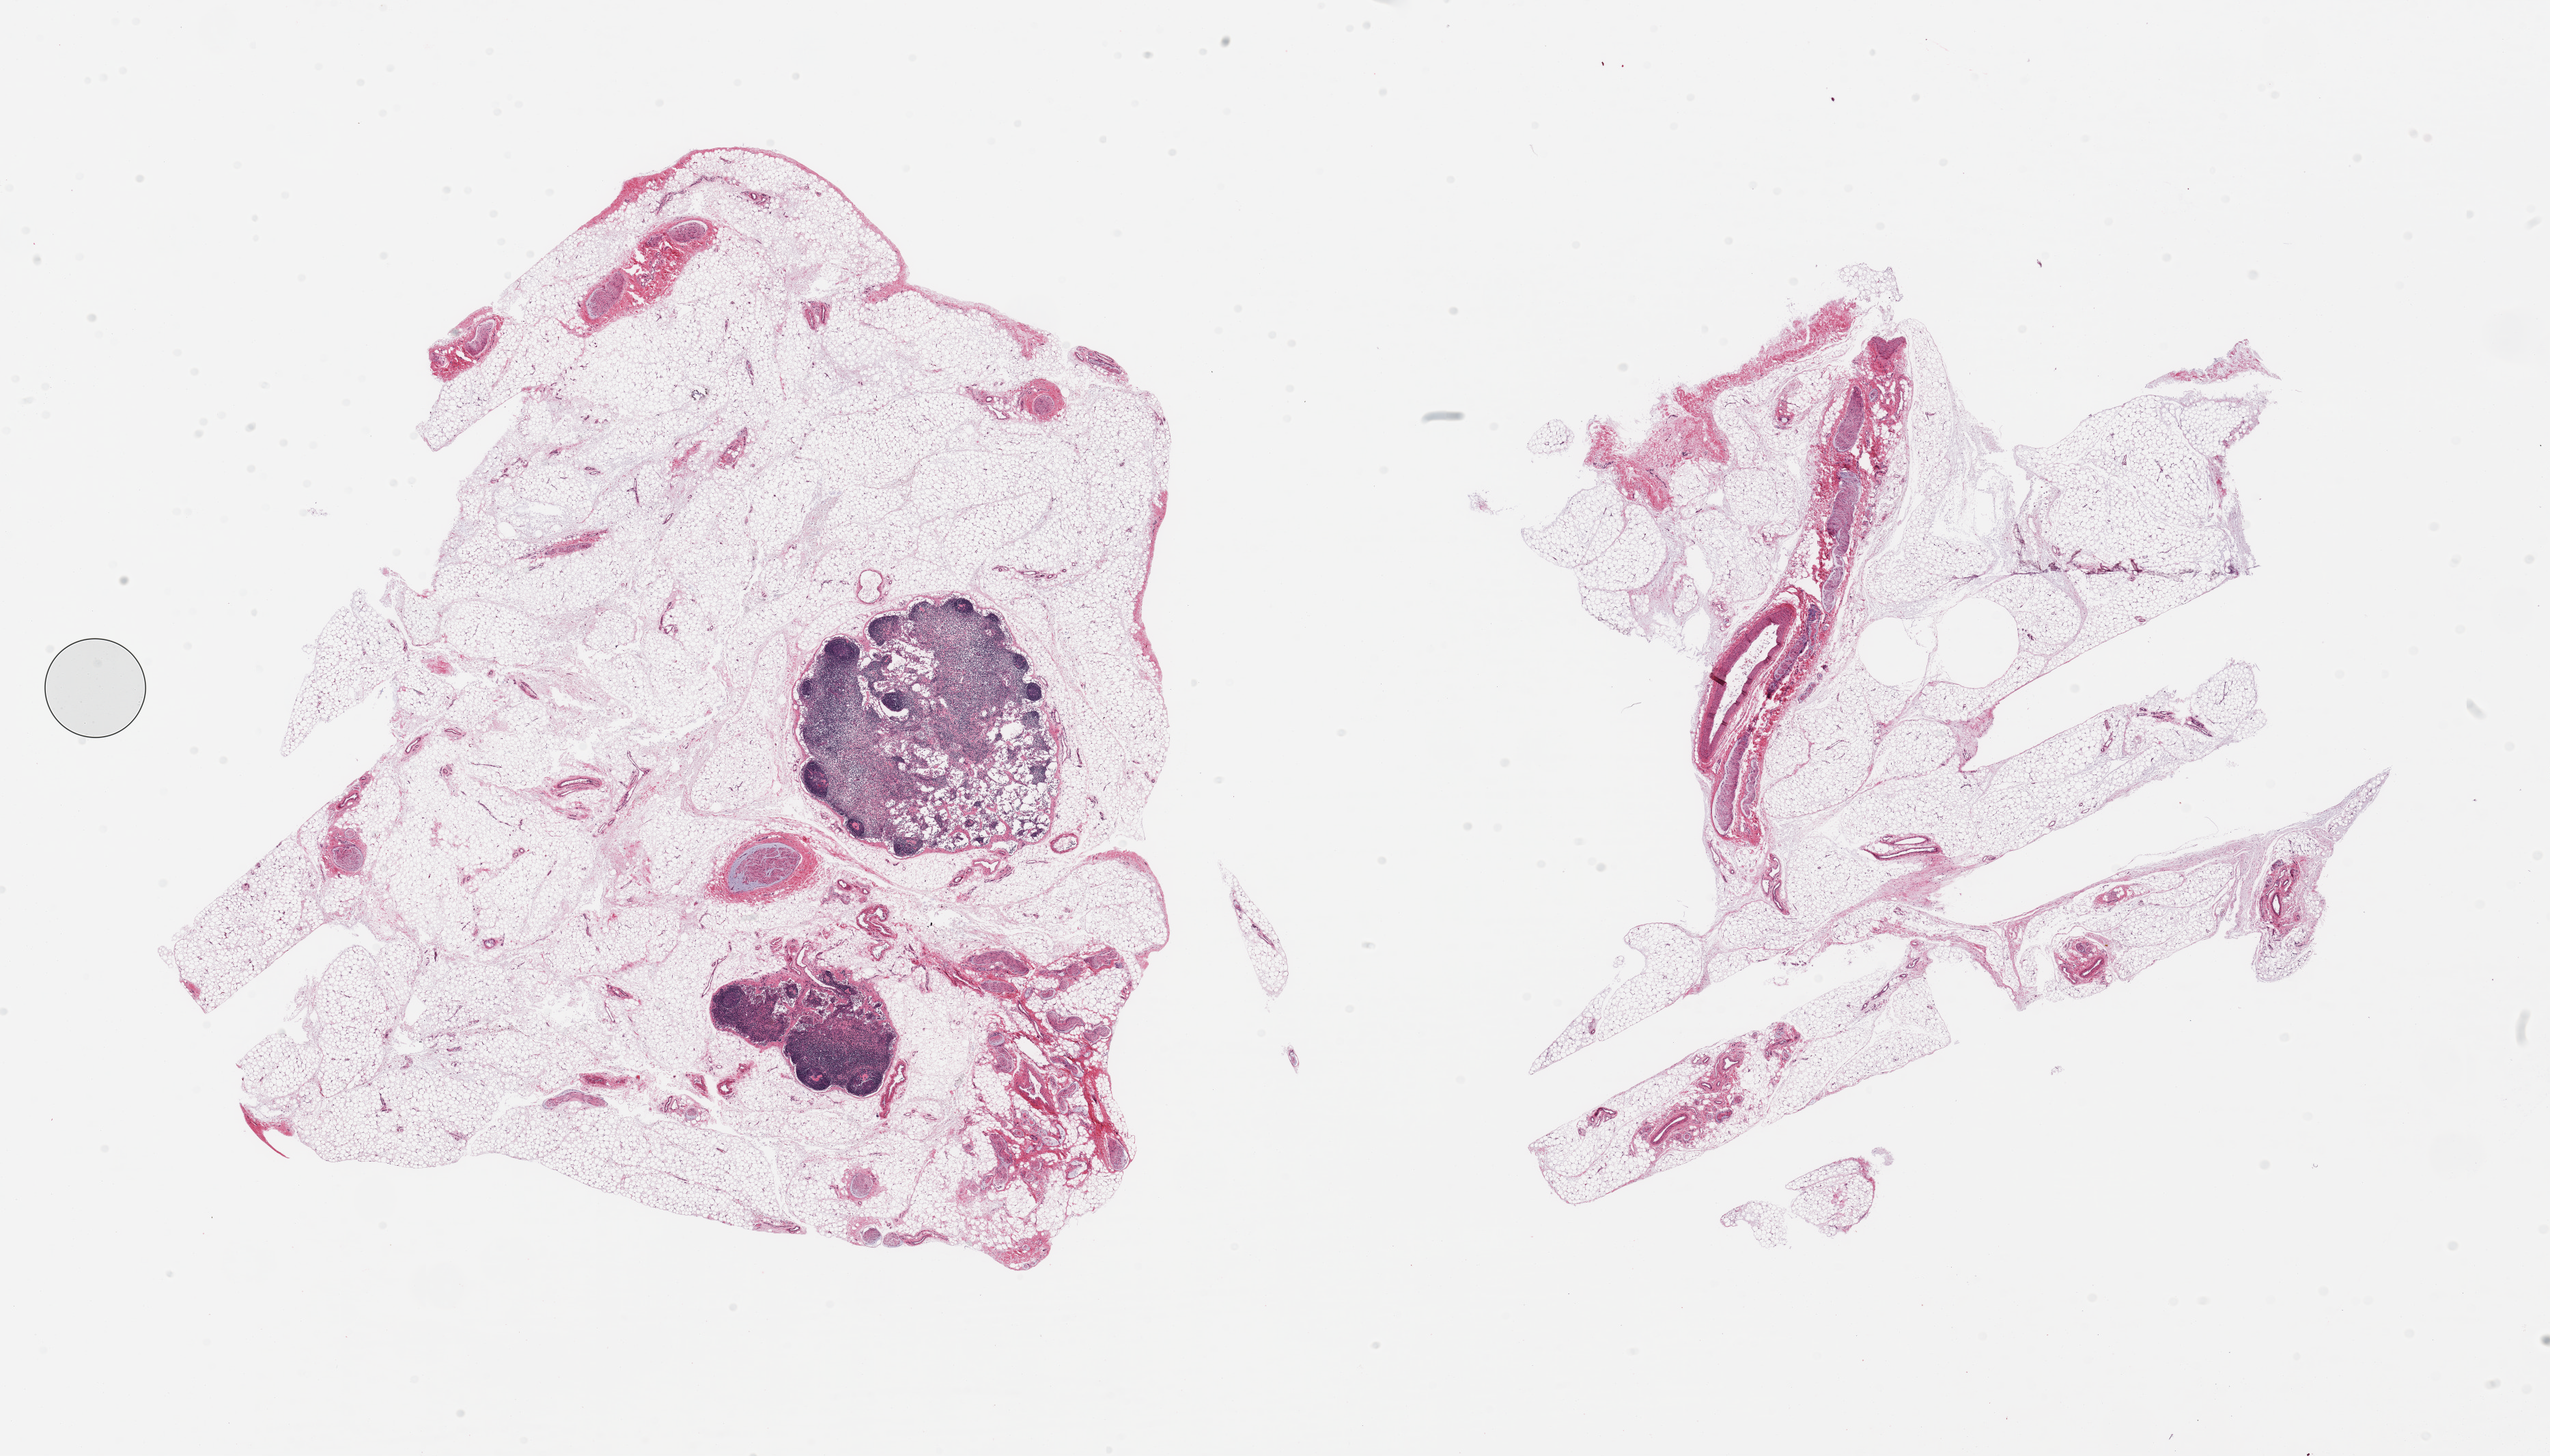
Whole-slide image, H&E stain, low-resolution overview of the scanned area, about 29.5 x 16.9 mm (from a 20x scan), PAXgene-fixed paraffin-embedded (PFPE) section, target tissue: omentum, tissue donor sample. Female donor.
Reviewer comment on this tissue sample: 2 pieces; mature adipose tissue with fibrovascular tissue and nerves; two small lymph nodes.